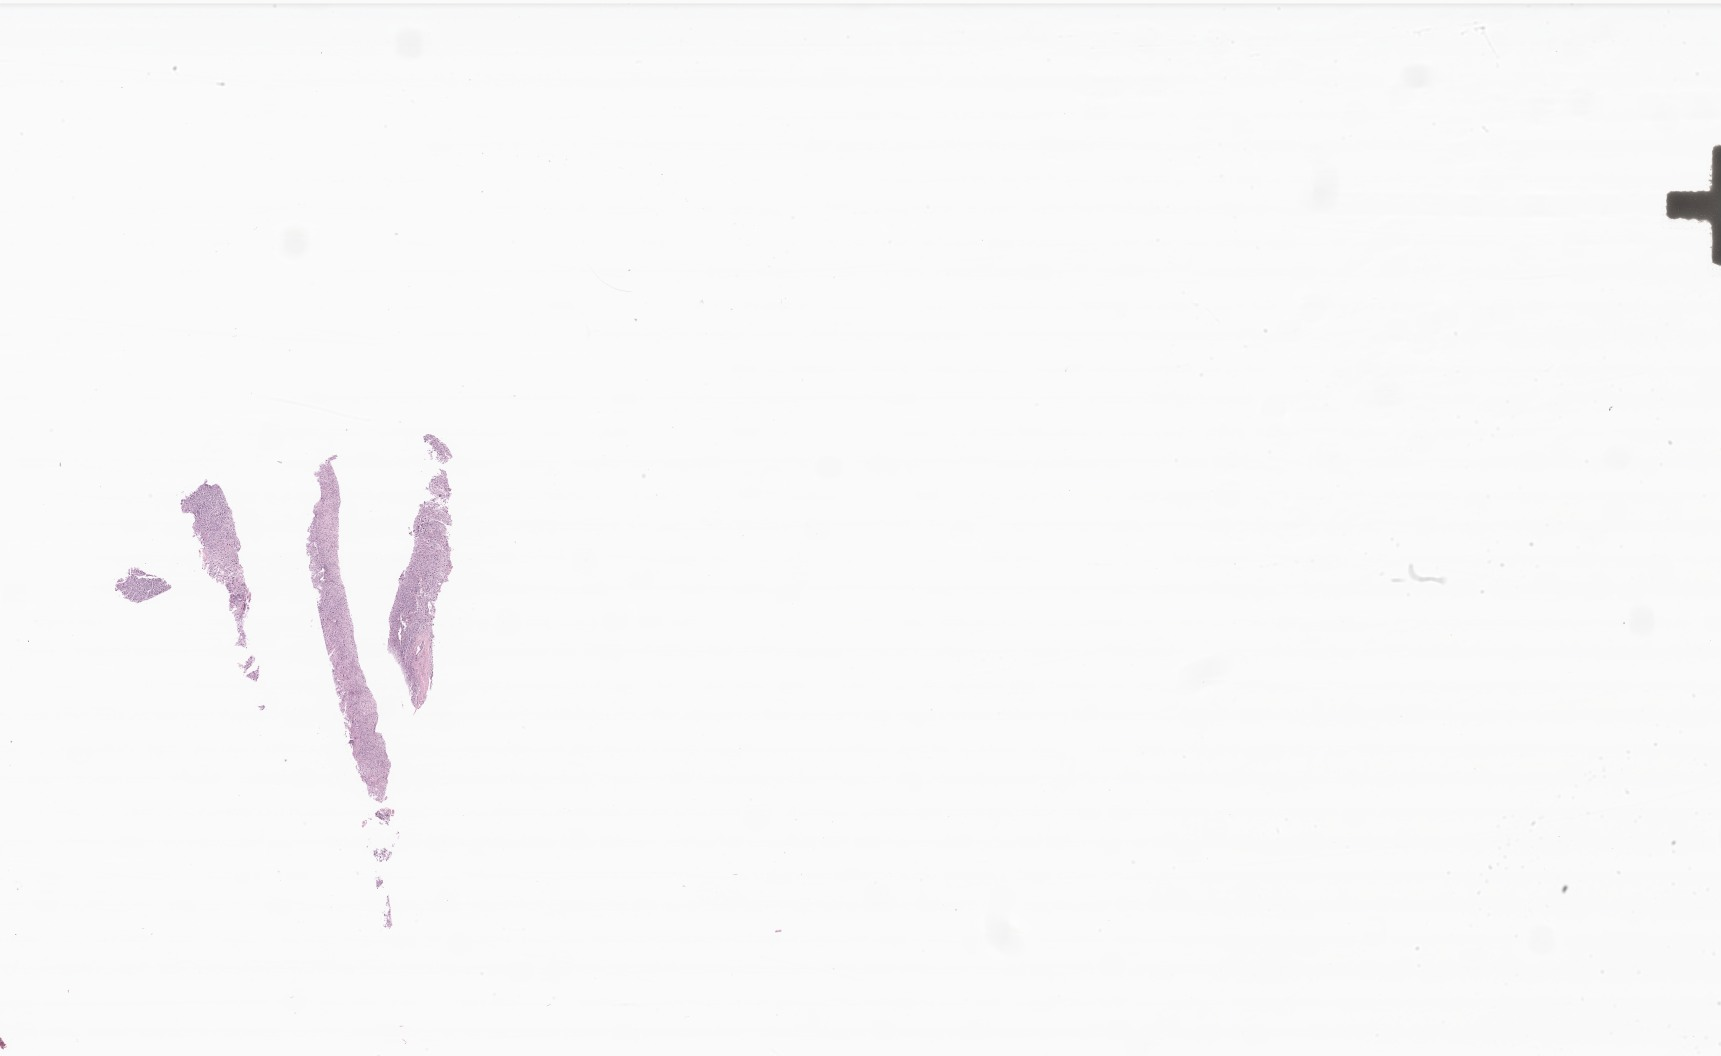
Whole-slide image, hematoxylin and eosin (H&E) stain of tumor tissue from the soft tissues of head and neck — a low-resolution overview of the entire scanned area, about 29.0 x 17.8 mm. Formalin-fixed paraffin-embedded section. Male patient, age 121 months (10 years 1 month).
- diagnosis (ICD-O-3 morphology term): Undifferentiated sarcoma